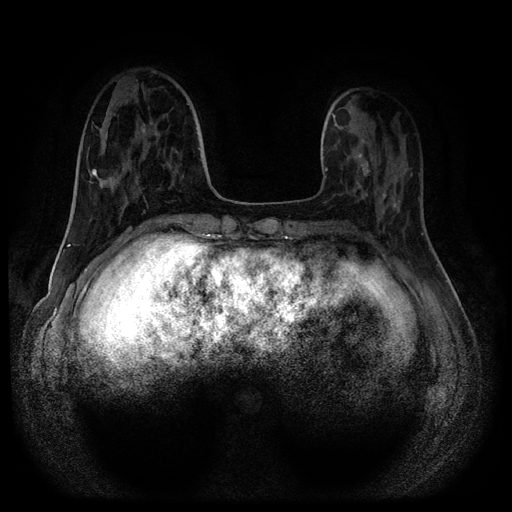
Breast MRI (dynamic contrast-enhanced, multi-phase), one axial slice. Dynamic contrast-enhanced series, time point 2 of 5 at this slice position (early post-contrast). 1.5 T. TE 2.7 ms, TR 5.4 ms. 512 × 512 image matrix, field of view 340 × 340 mm. Female patient, age 40 years.
Structures marked on this image (semi-automatic segmentation, software-assisted and operator-edited):
- breast lesion (labelled benign in the annotation): bounding box (x1, y1, x2, y2) in pixels: (352, 152, 375, 201)